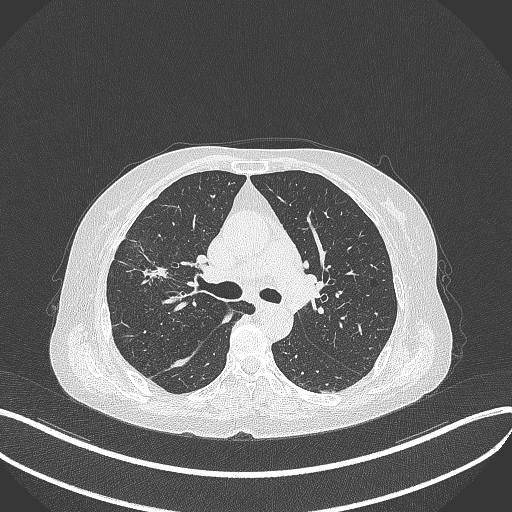
Chest CT, one axial slice. Position 254 of 429 along the scan axis. Reconstruction kernel B70f. 120 kVp. Lung window (W 1500 / L -600 HU). 1 mm slice thickness. 512 × 512 image matrix, field of view 400 × 400 mm. Female patient, age 69 years. Case-level facts recorded for this patient, not image findings: clinical TNM (as recorded): T1b N3 M0.
Annotated regions visible in this slice (bounding box drawn by a radiologist):
- lung tumour (recorded histology: small cell carcinoma): box from (x=133, y=253) to (x=180, y=284) px